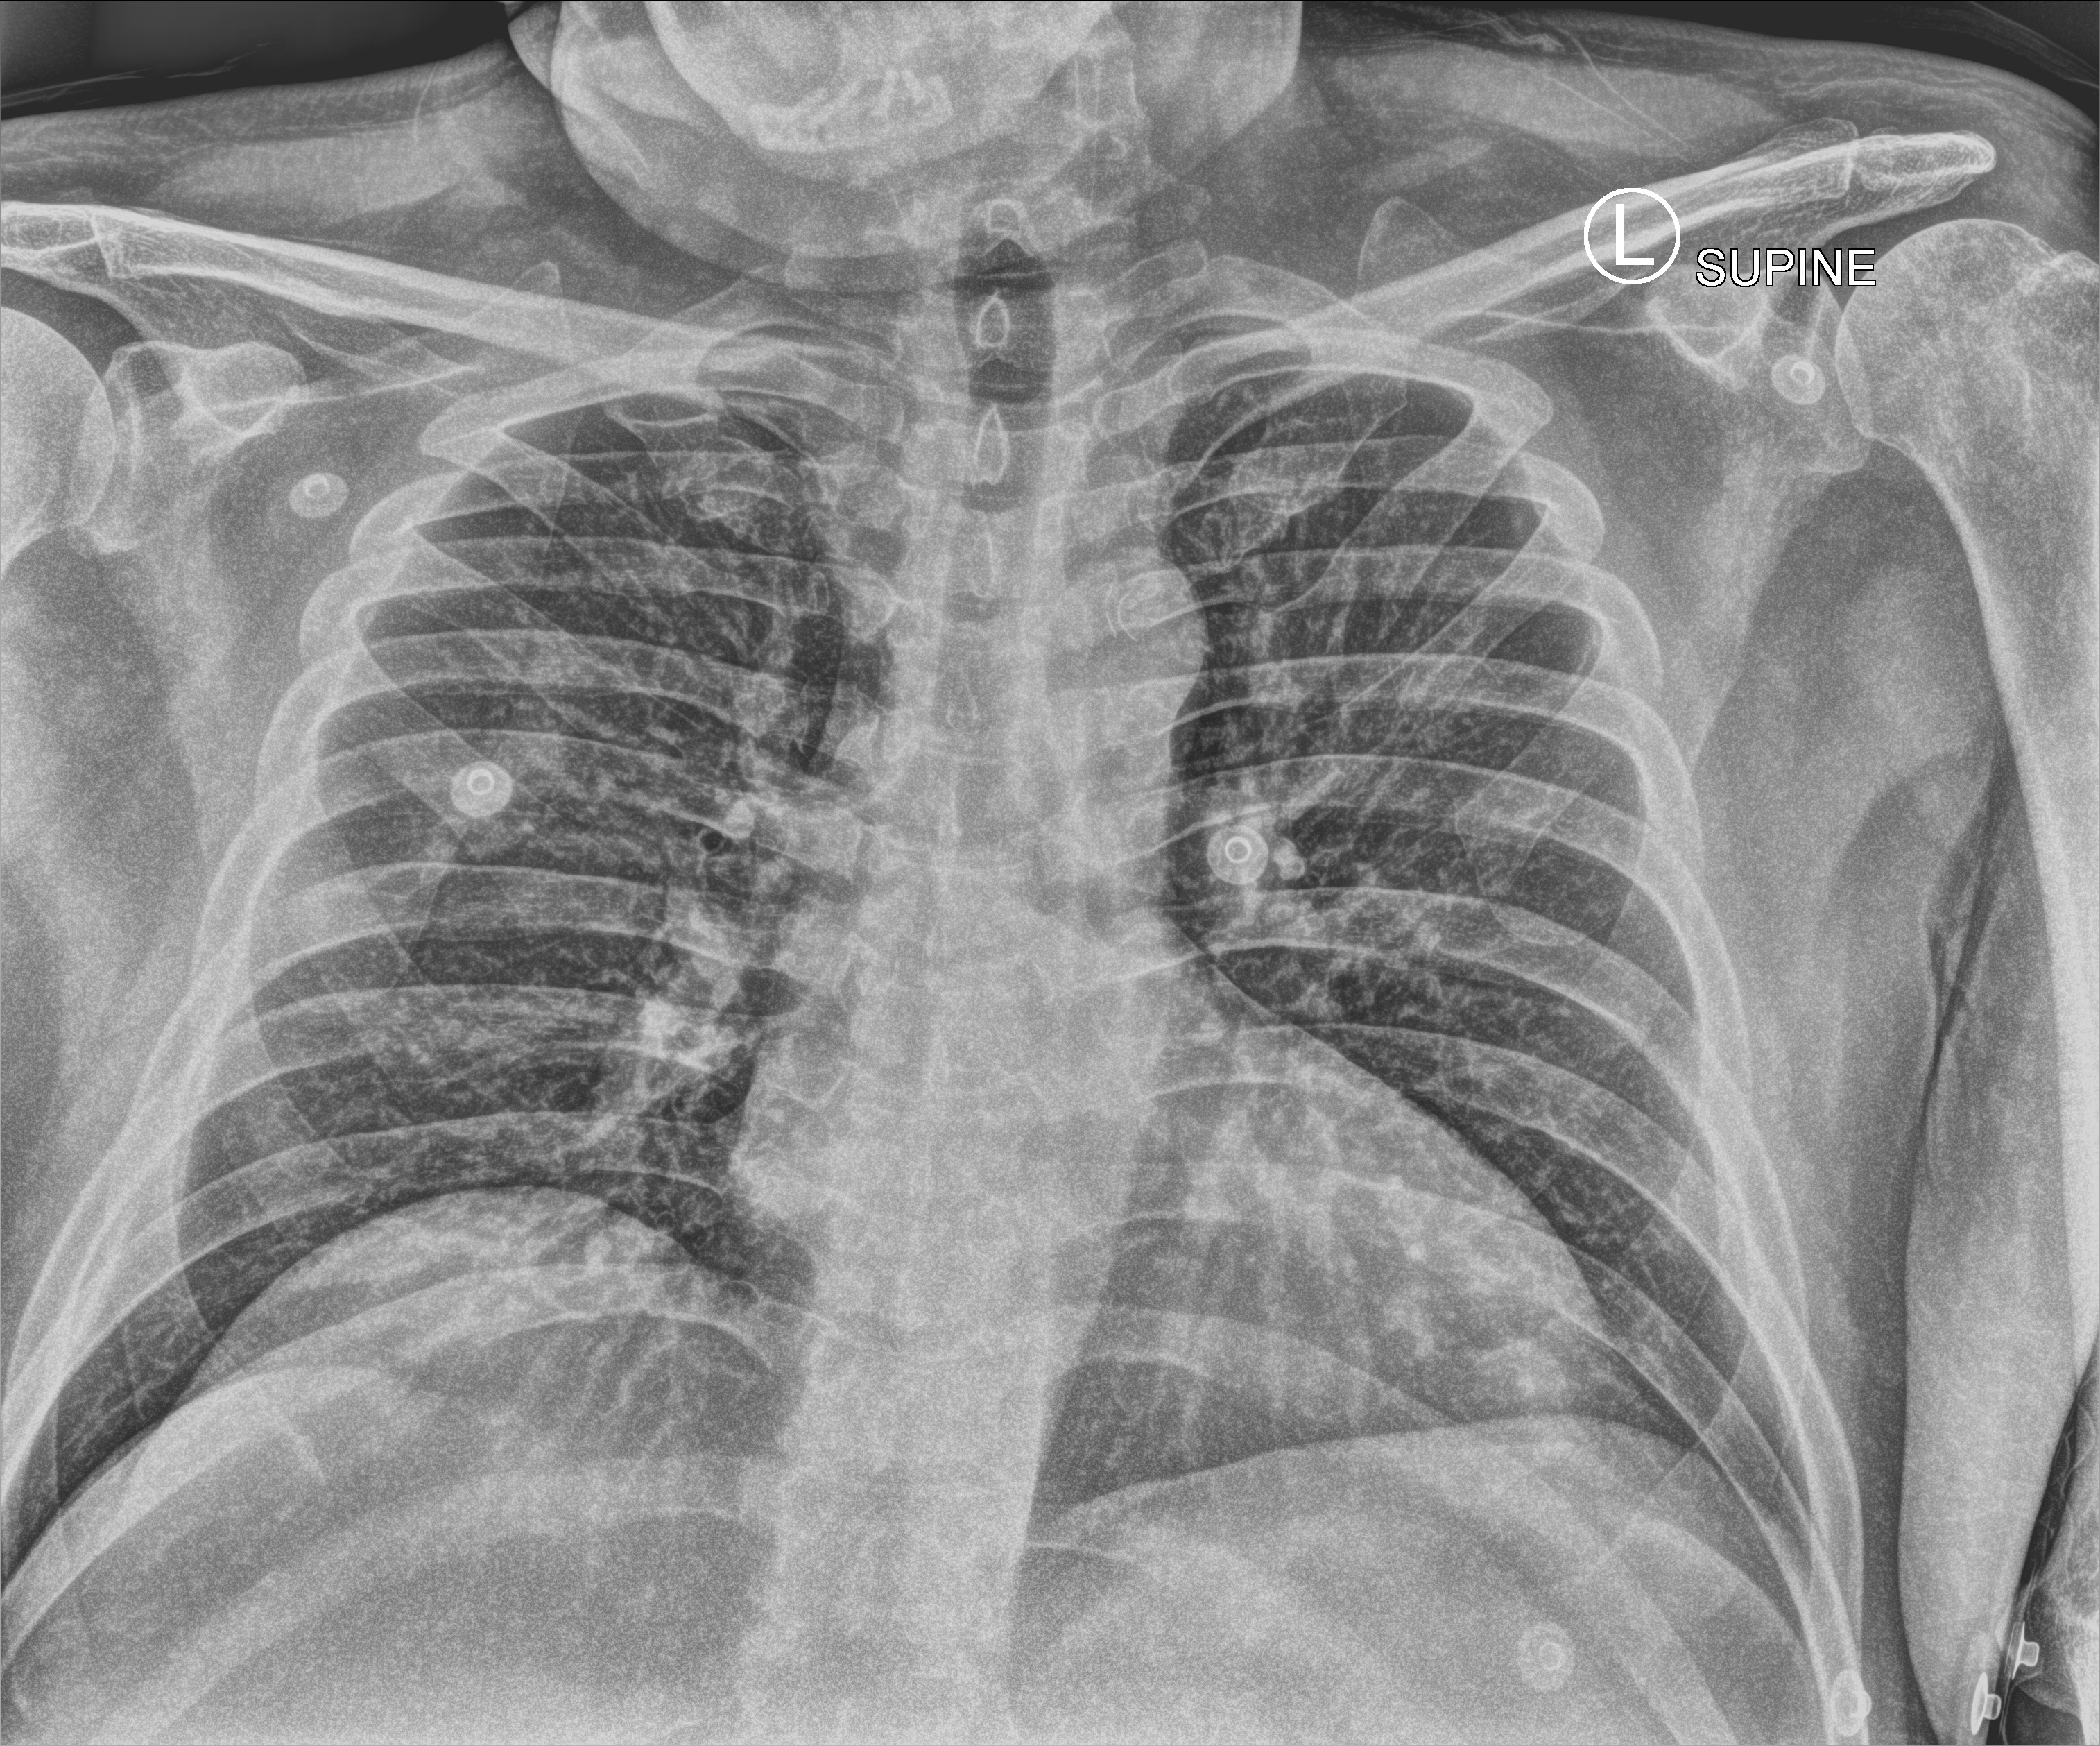
Bedside chest radiograph (computed radiography); anteroposterior (AP) projection. Patient hospitalised with COVID-19; male, aged 18–59 years.
Admission-level facts for this patient (not findings on this image; timing relative to this image not recorded): length of hospital stay: 2 days; mechanically ventilated during this hospital stay: no; admitted to intensive care during this hospital stay: no.